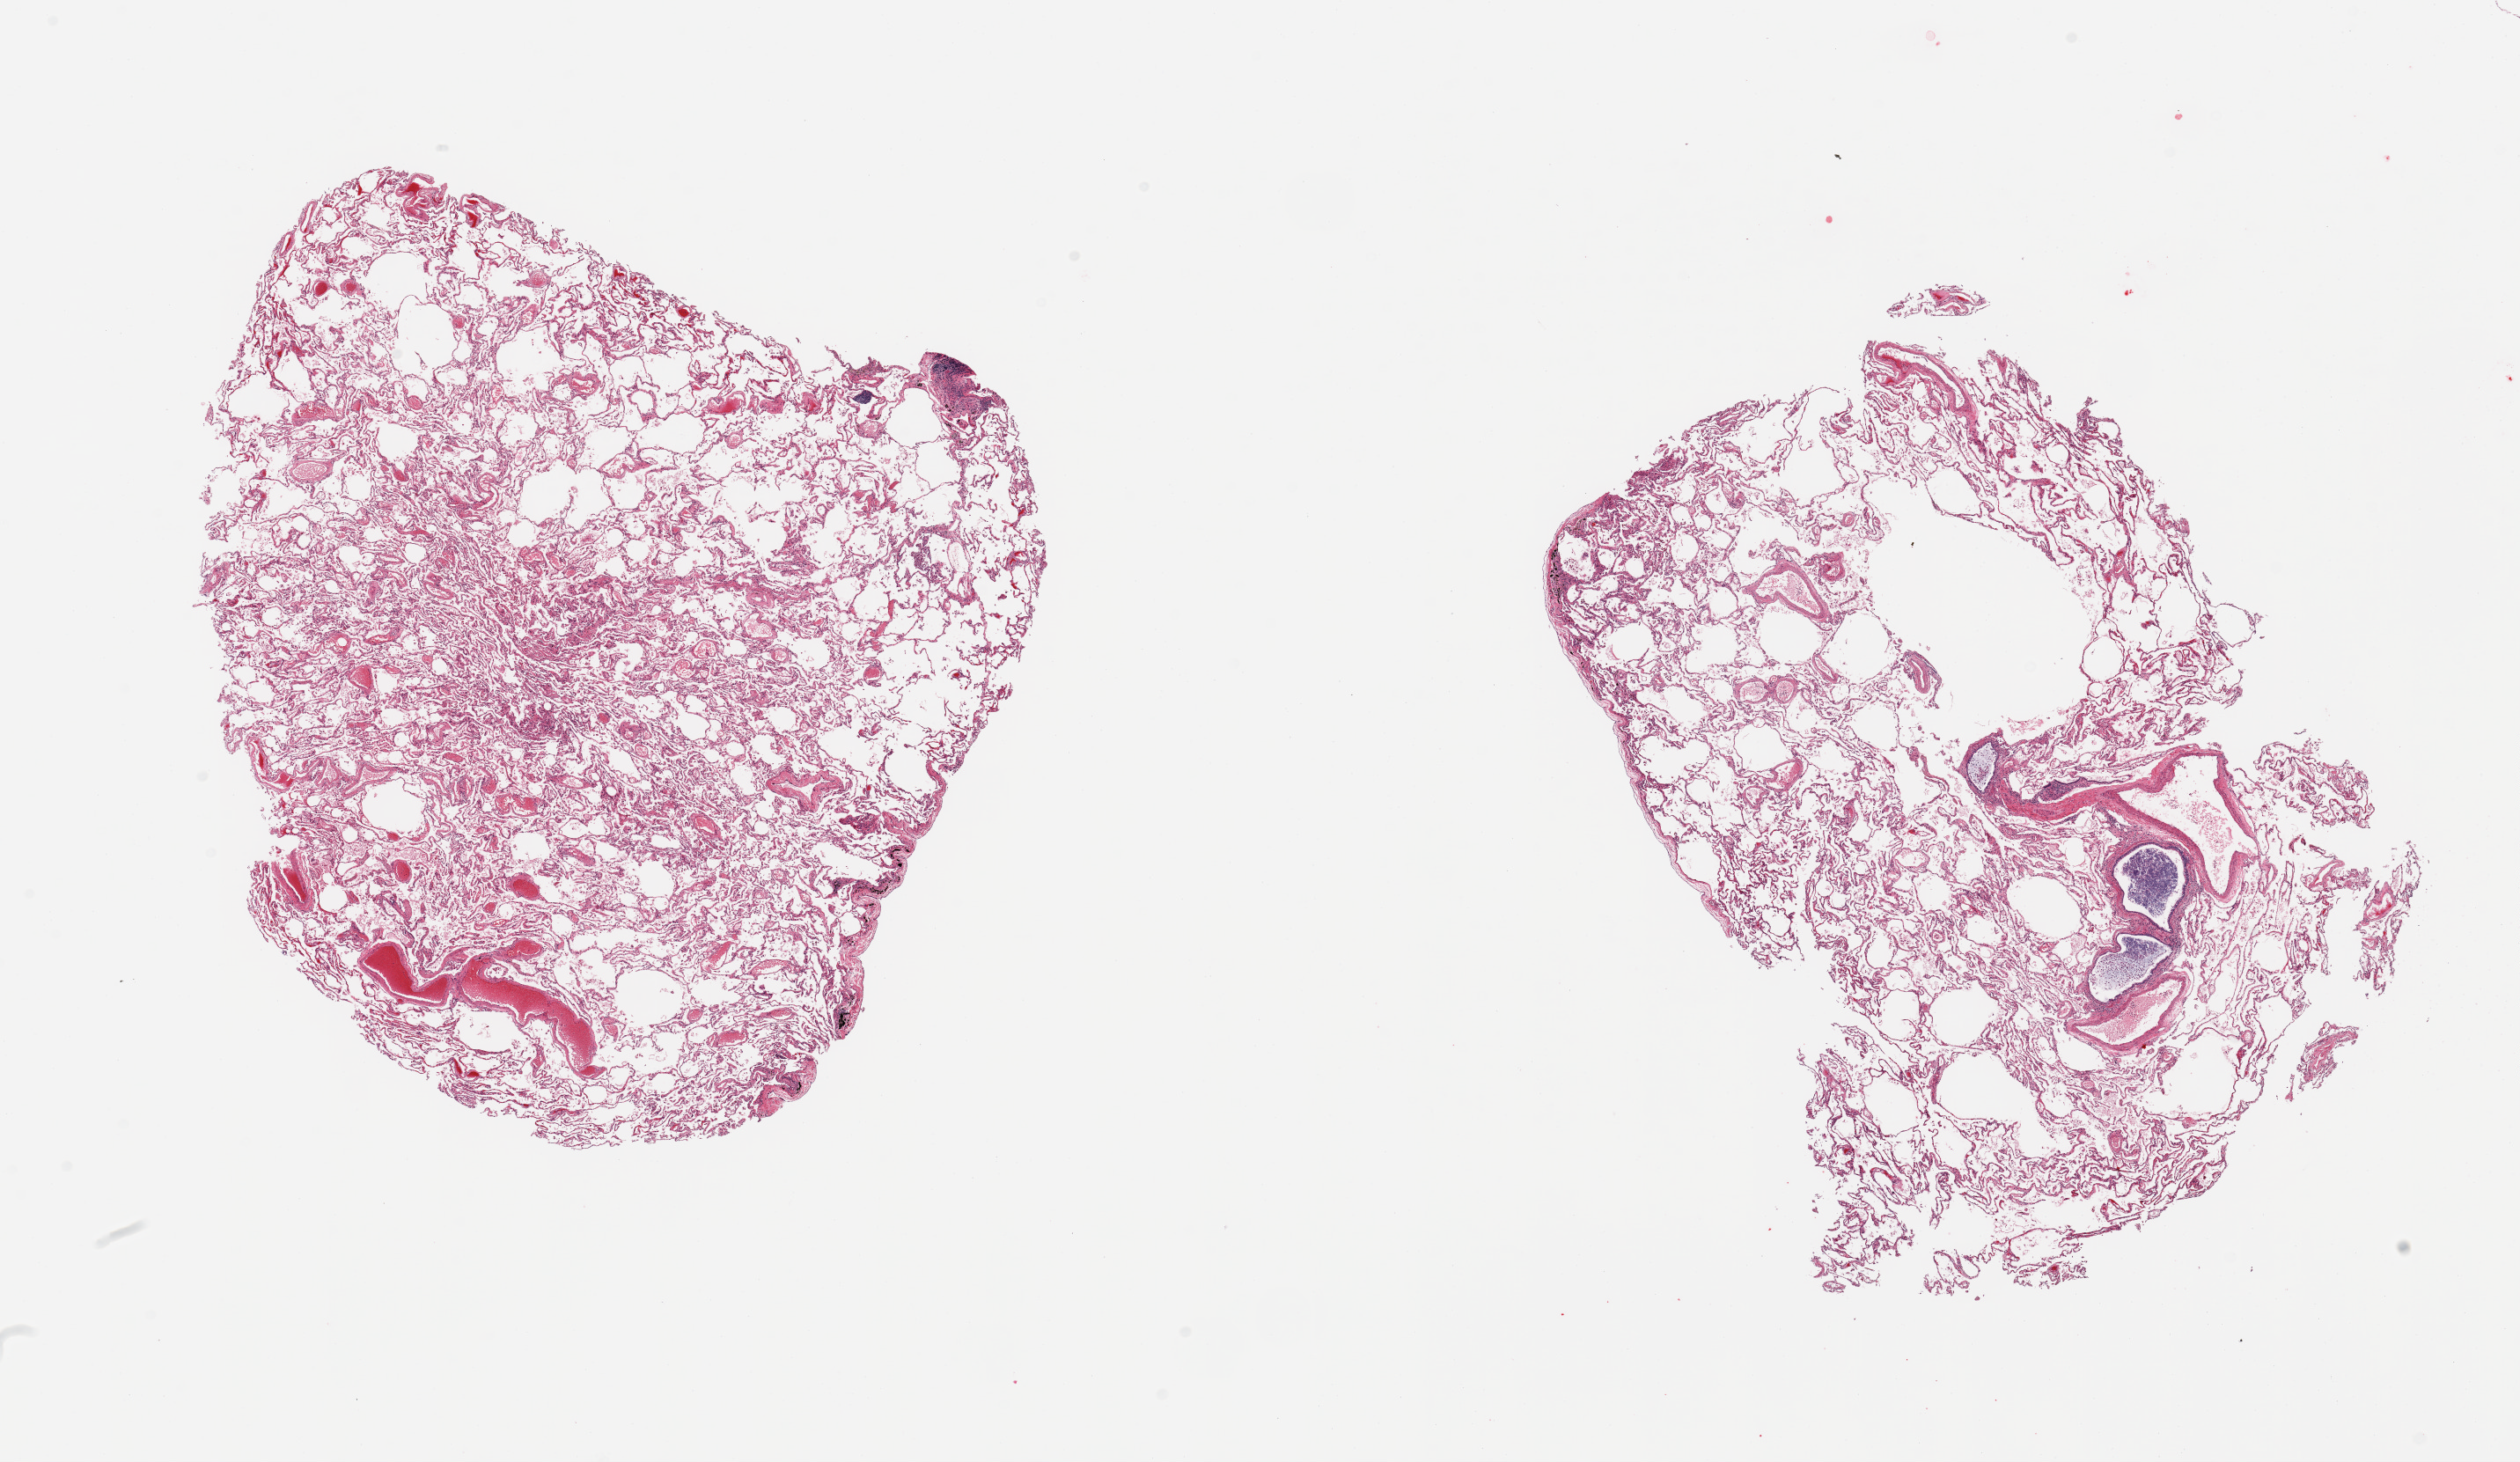
Hematoxylin and eosin (H&E) whole-slide image — shown as a low-resolution overview of the whole scanned area (about 22.6 x 13.1 mm). PAXgene-fixed, paraffin-embedded tissue. Section of lung (target tissue). Donor tissue sample. Donor: male.
• reviewer comment on this tissue sample: 2 pieces; prominent diffuse emphysema